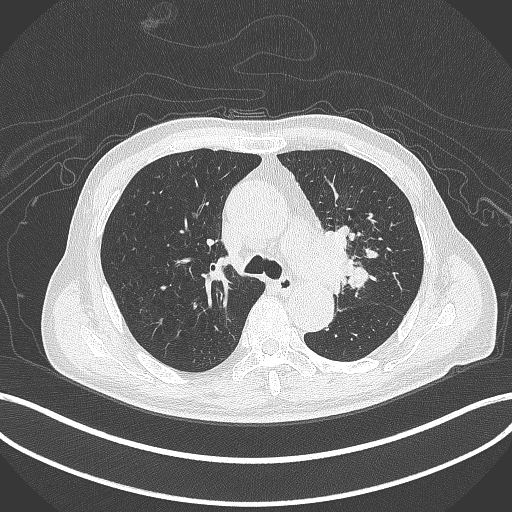
Chest CT, one axial slice; position 289 of 417 along the scan axis; reconstruction kernel B70f; 120 kVp; lung window (W 1500 / L -600 HU); 1 mm slice thickness; 512 × 512 image matrix. Male patient, age 77 years. From the clinical record (not read from this slice): clinical TNM (as recorded): T3 N1 M0.
Annotated regions visible in this slice (rectangle marked by the reading radiologist):
- lung tumour (recorded histology: adenocarcinoma): bounding box <312,228,357,290> (left, top, right, bottom; pixels)